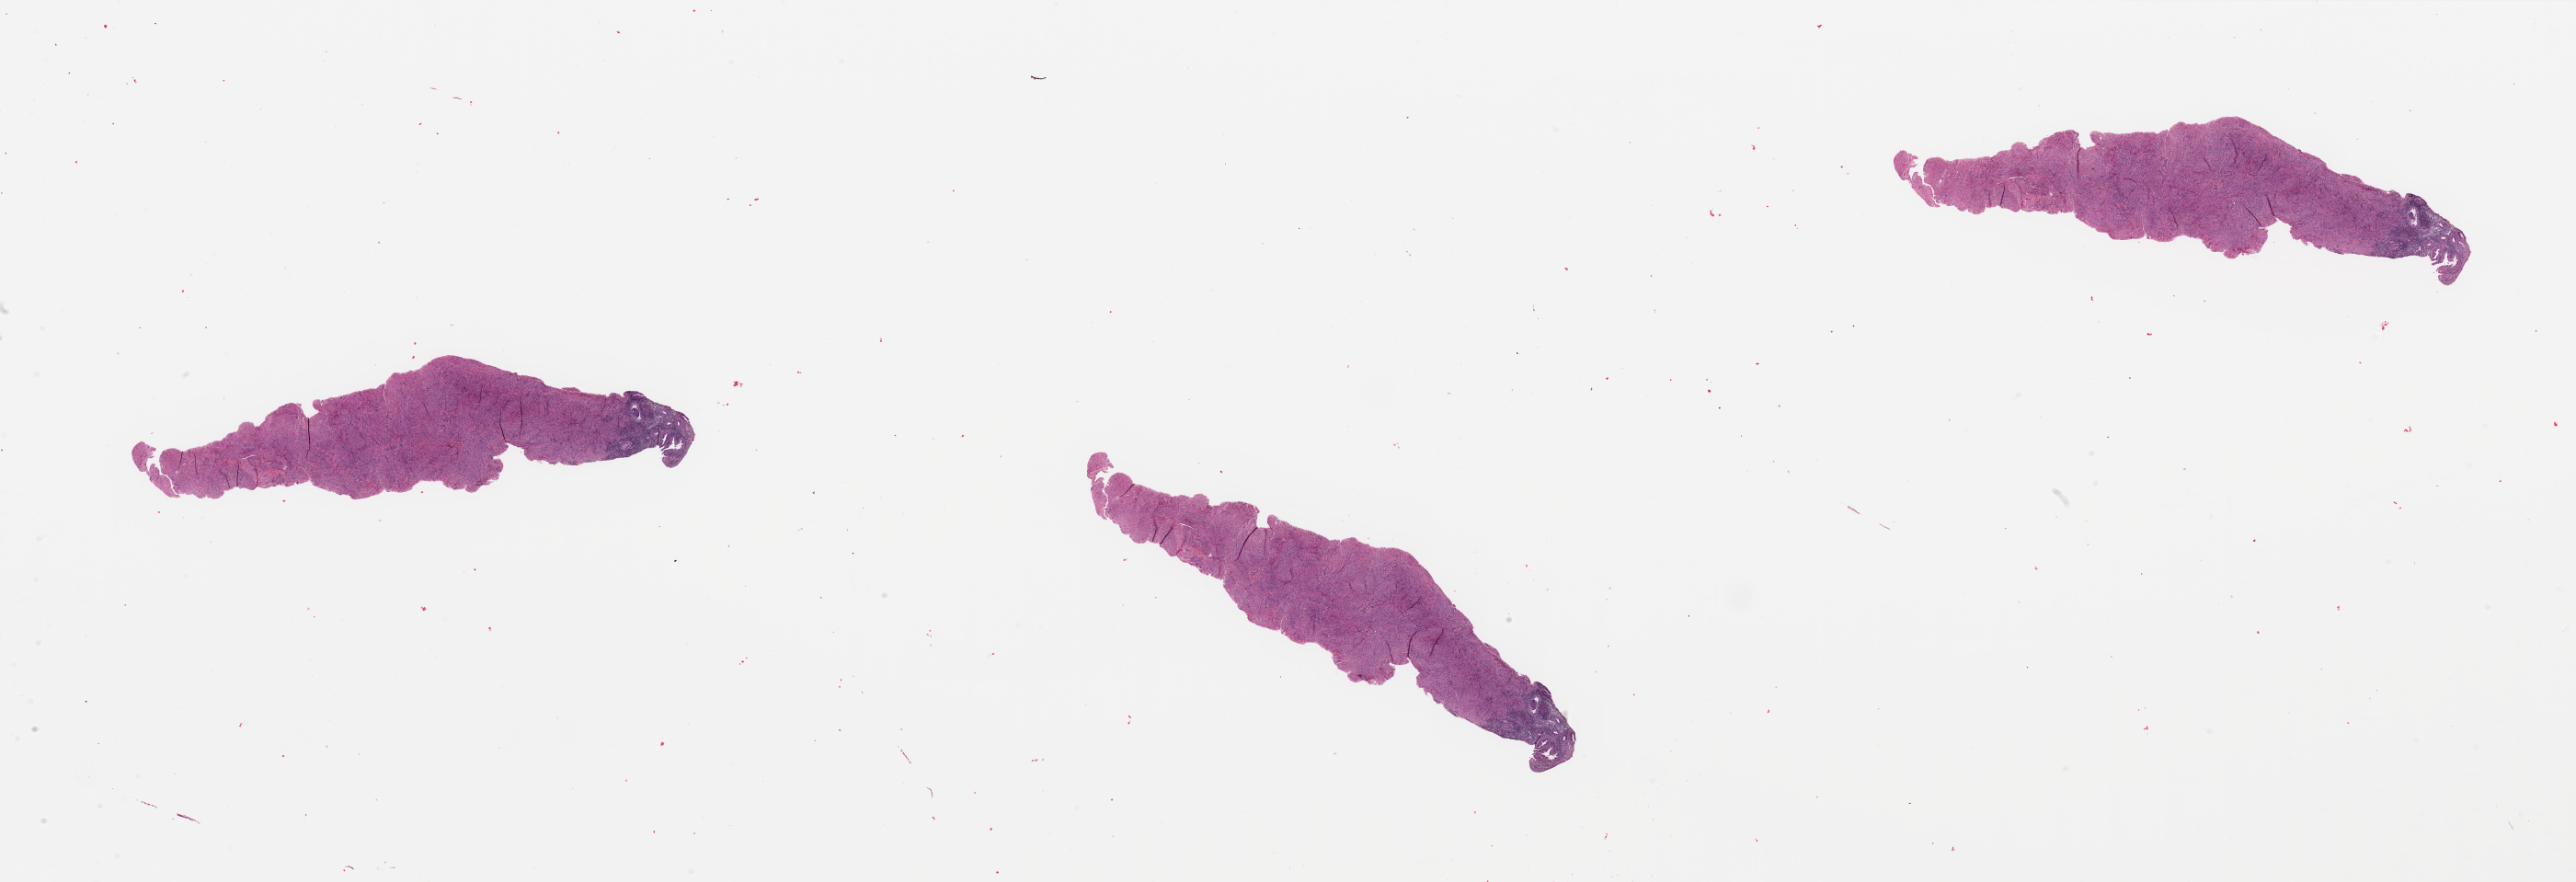
Whole-slide histology image, H&E — shown as a low-resolution overview of the whole scanned area (about 44.3 x 15.2 mm), normal (non-tumour) tissue sample, sampled site: uterus. Female, 39 y/o.
• this section: normal (non-tumour) tissue from the same patient
• patient diagnosis: Endometrioid adenocarcinoma, NOS